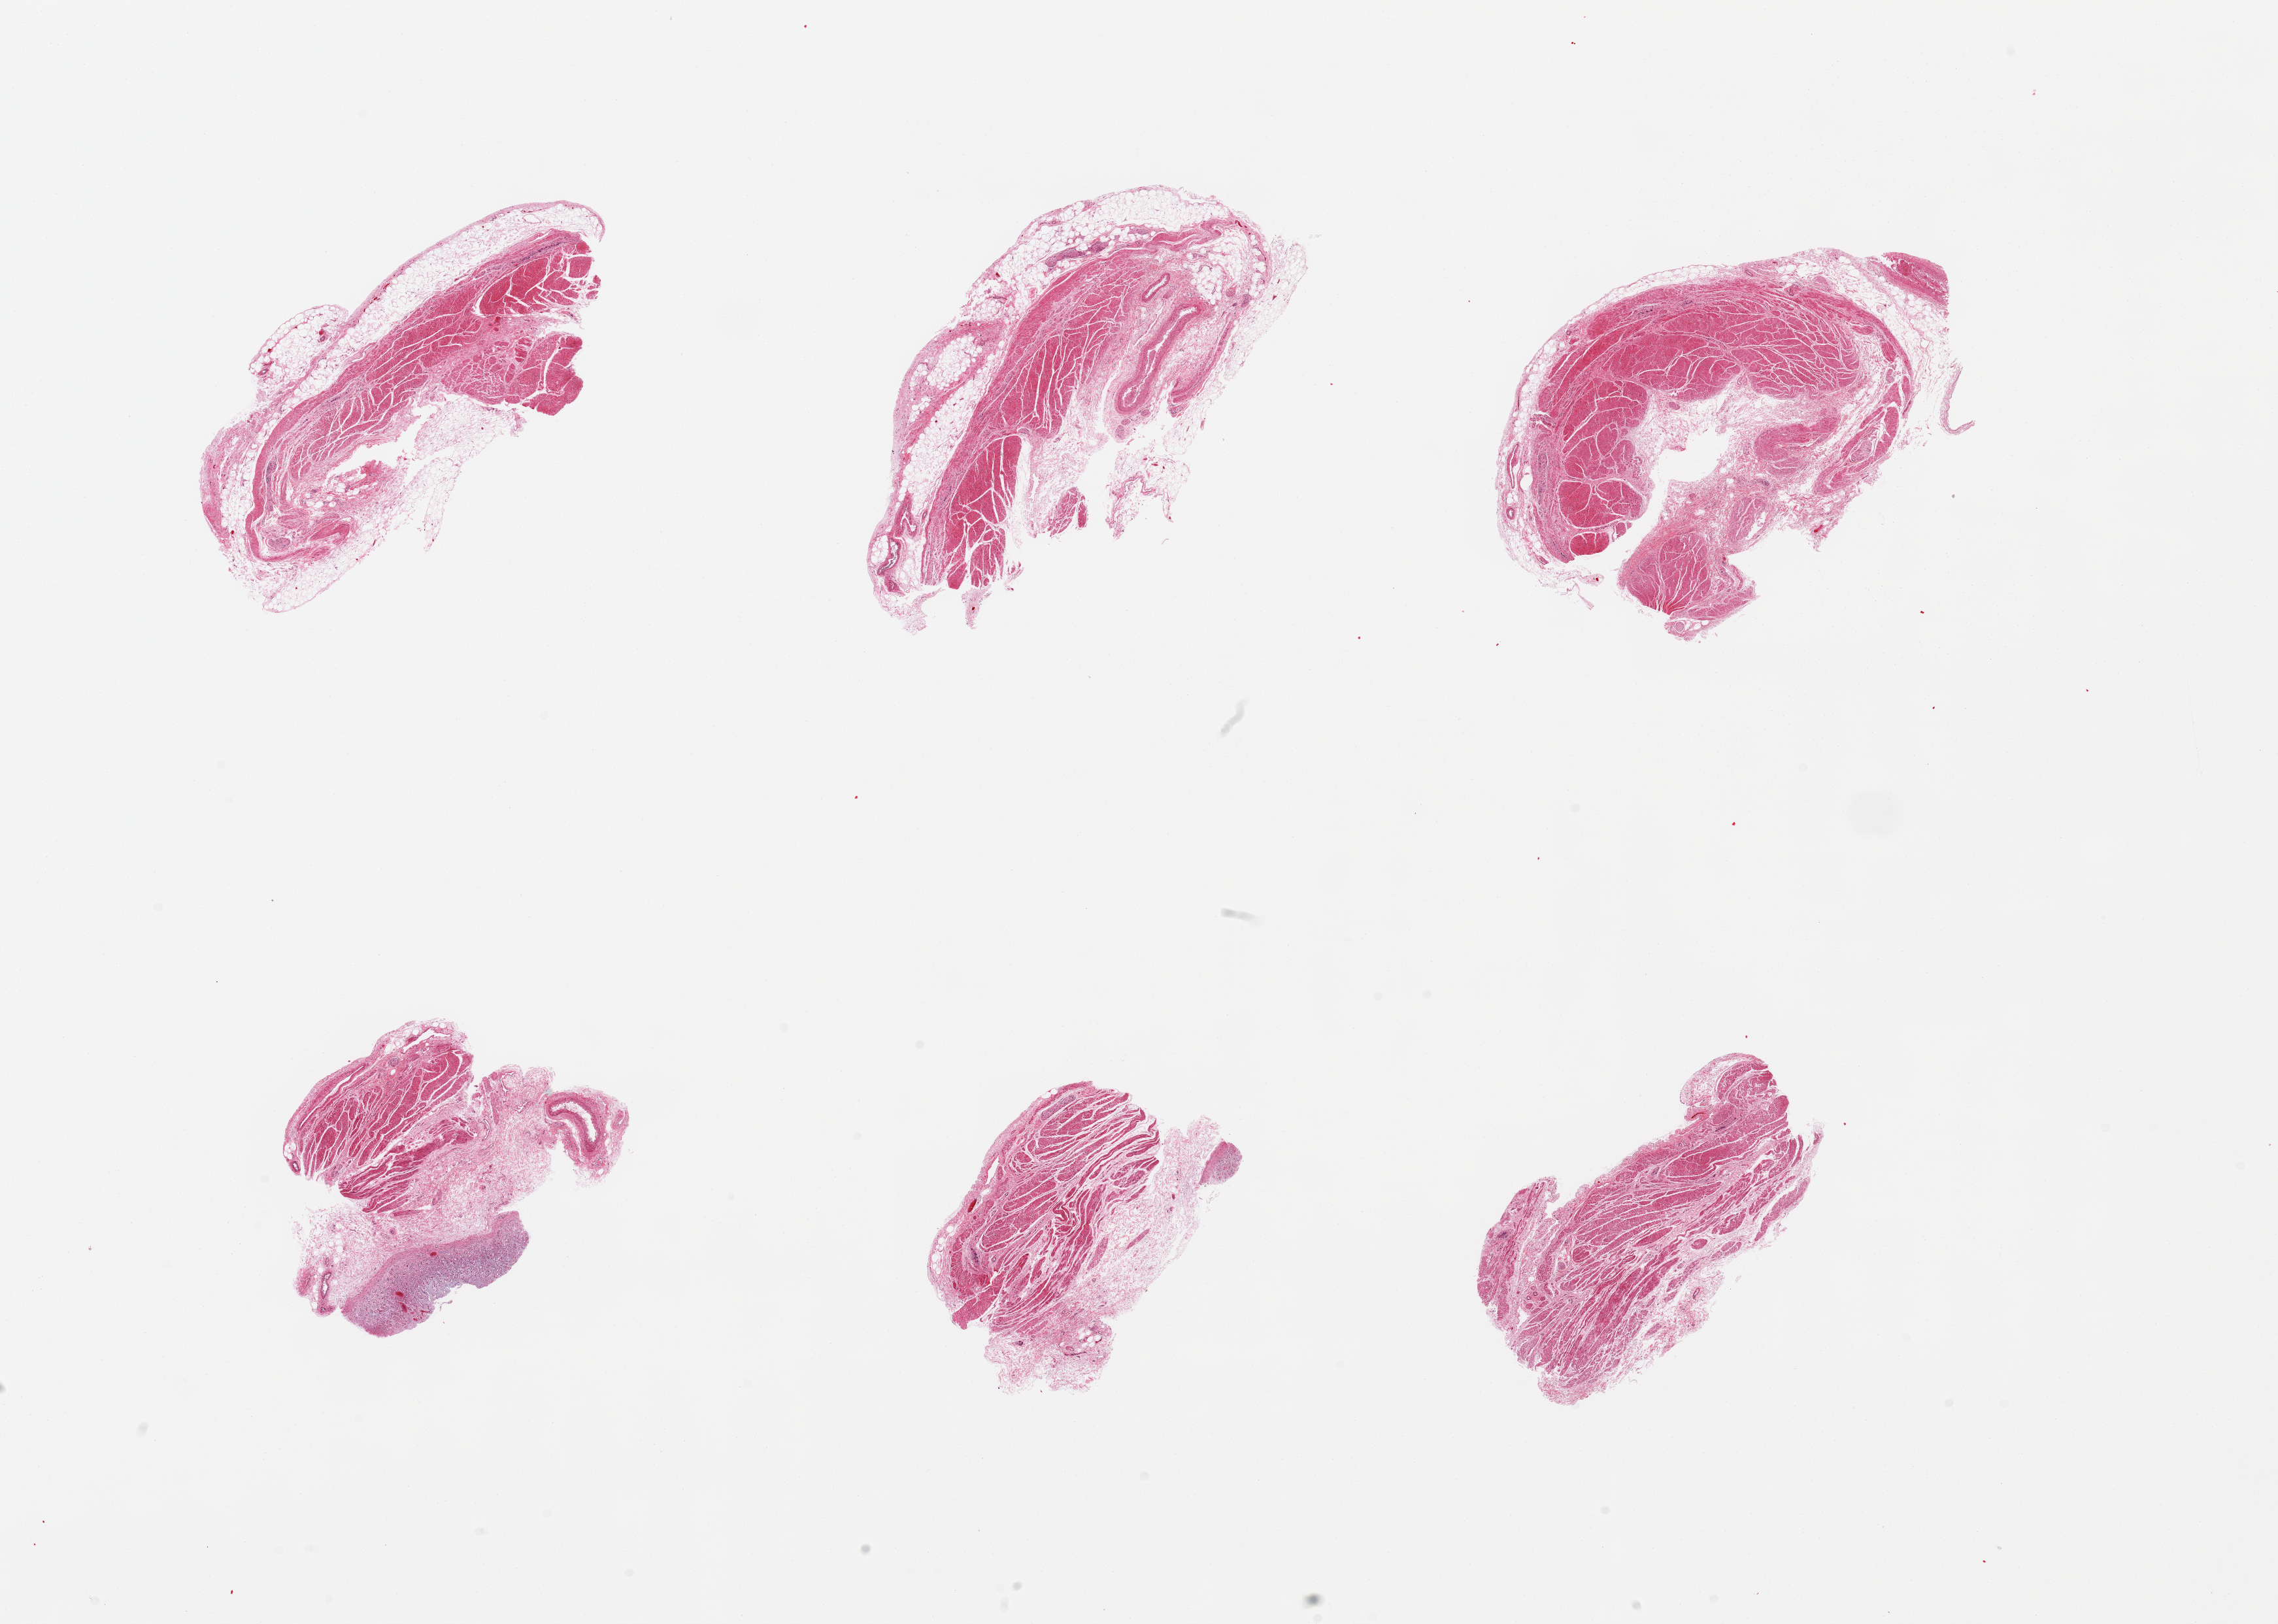
H&E whole-slide image, a low-resolution overview of the entire scanned area, about 27.6 x 19.7 mm, PAXgene-fixed, paraffin-embedded tissue, target tissue: stomach, donor tissue sample. Male donor.
• reviewer comment on this tissue sample: 6 pieces, mucosa largely sloughed/autolyzed; one surviving focus is markedly autolyzed